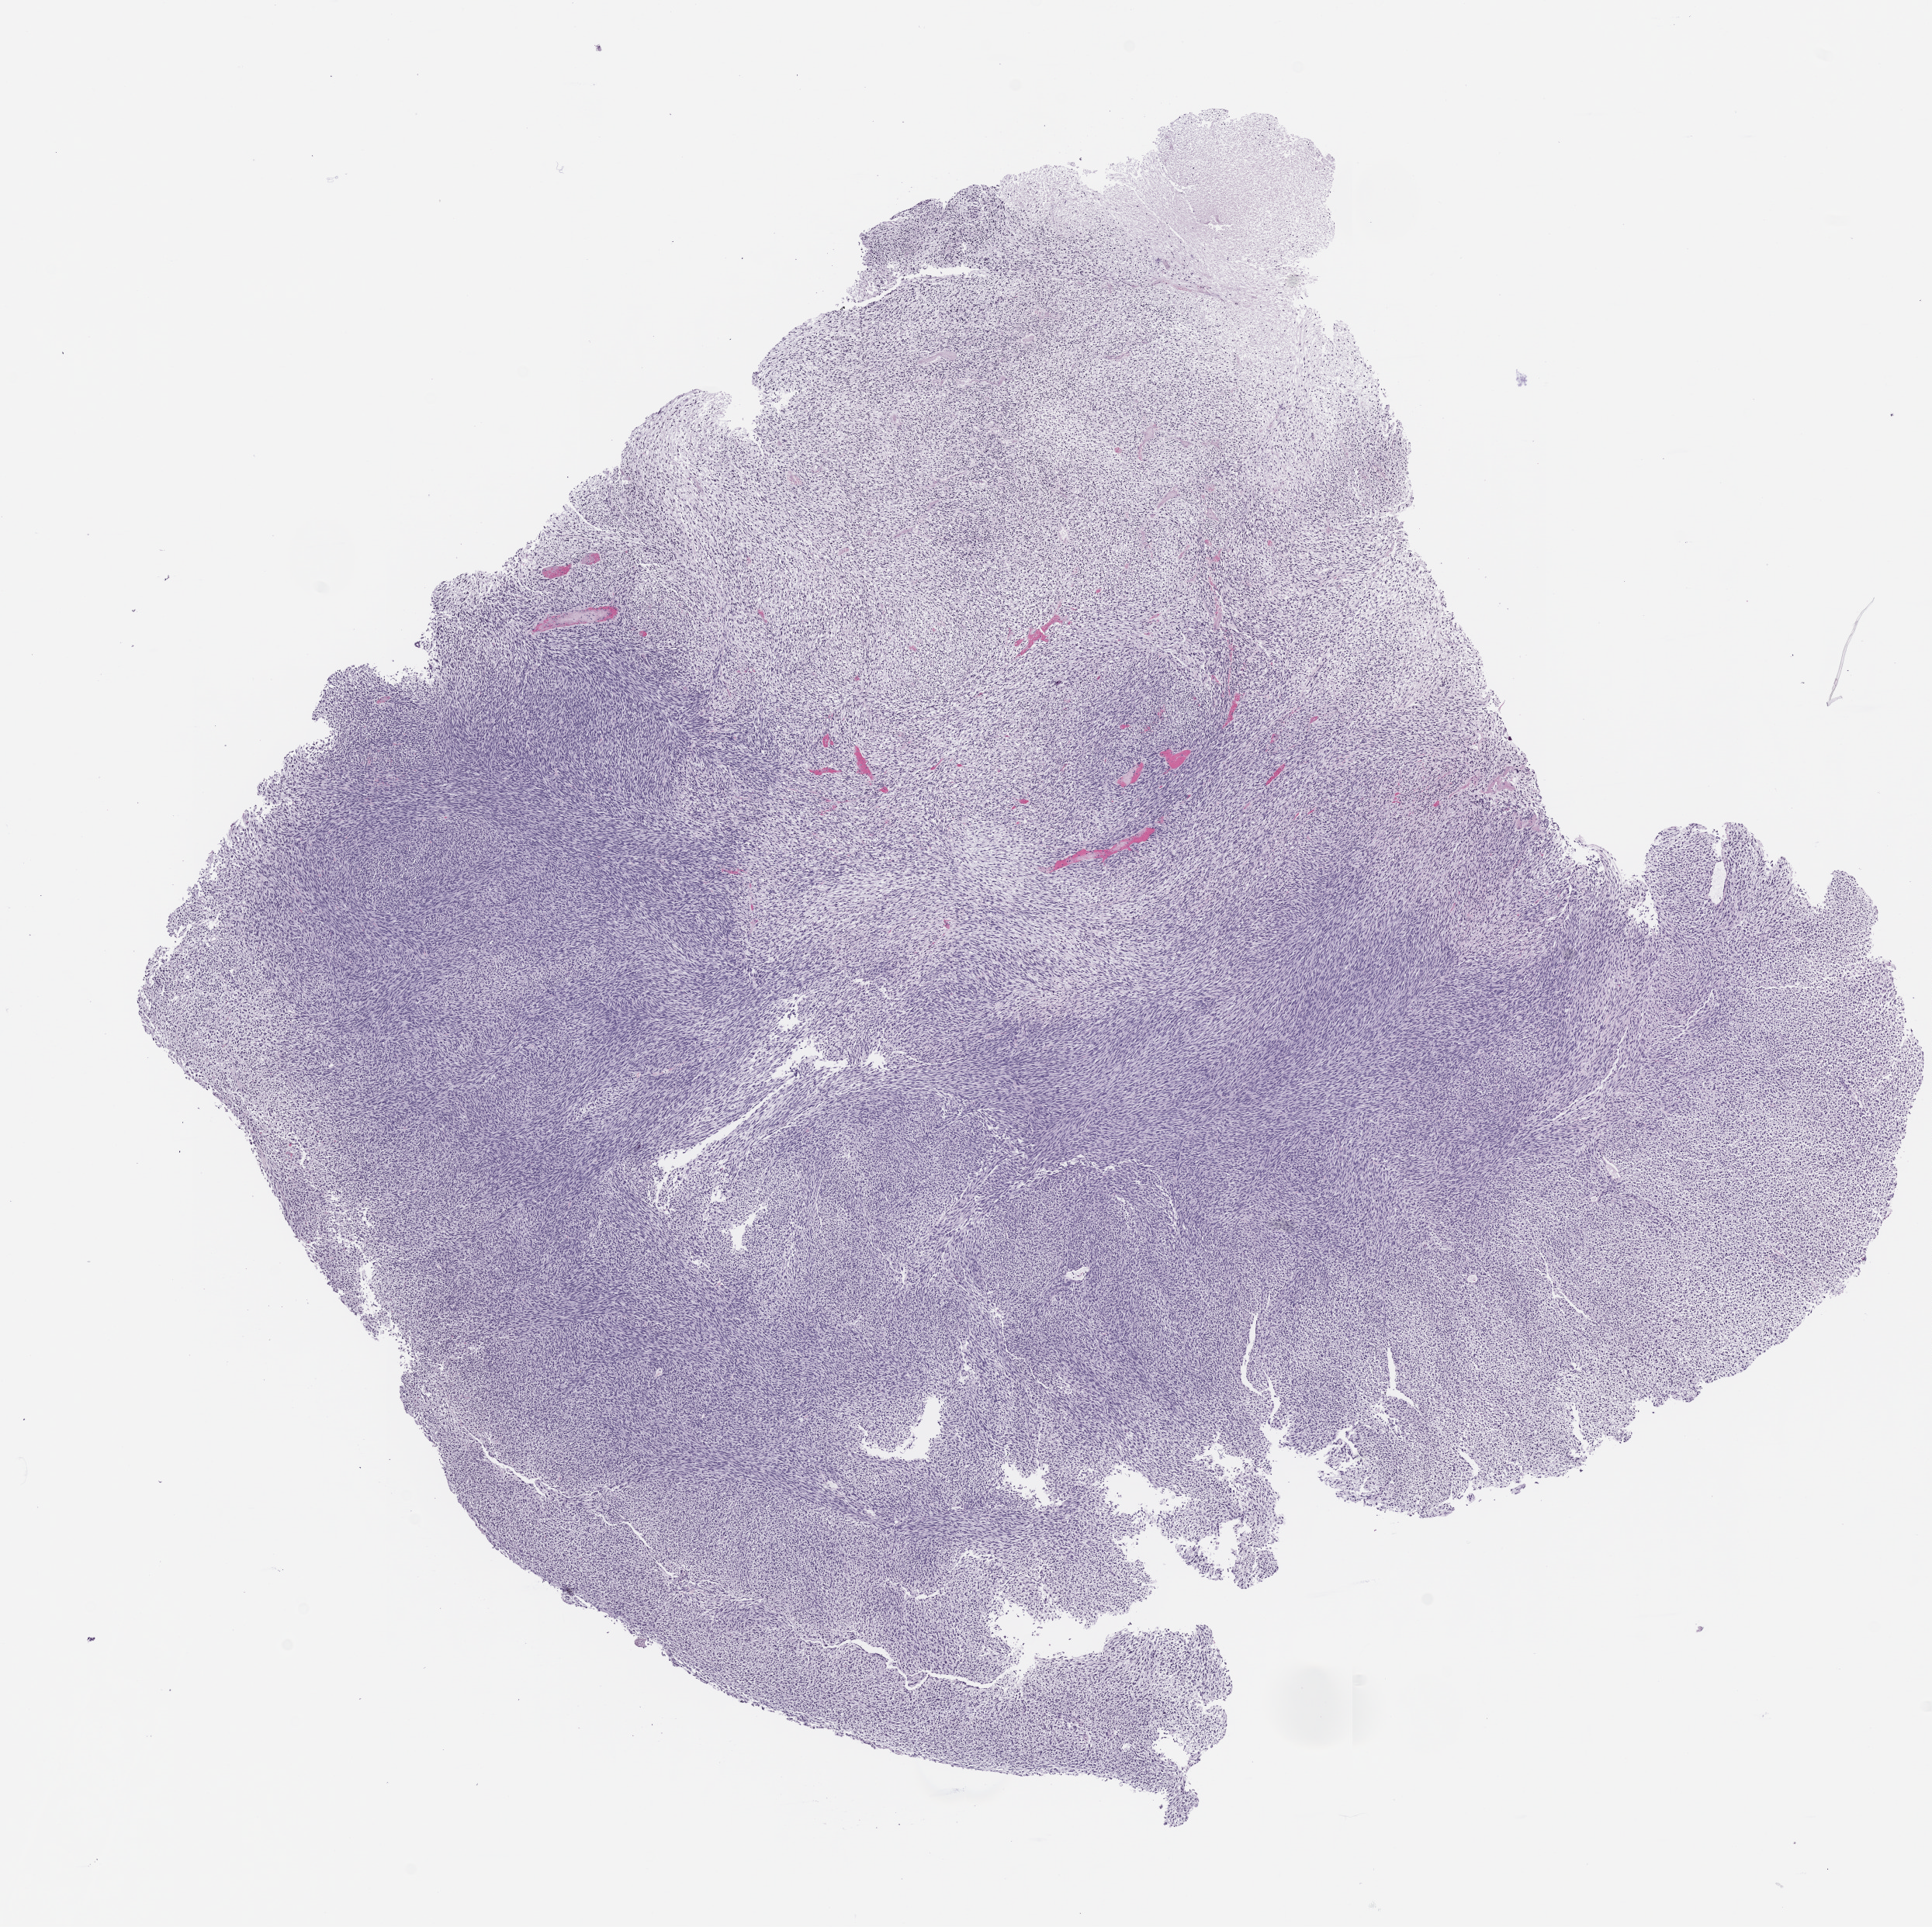
Whole-slide image, haematoxylin and eosin: patient-derived xenograft (human tumor grown in a mouse), passage 2 — shown as a low-resolution overview of the whole scanned area (about 10.0 x 10.0 mm). Formalin-fixed paraffin-embedded section. Originating tumor site category: musculoskeletal.
Originating patient diagnosis: Synovial Sarcoma.